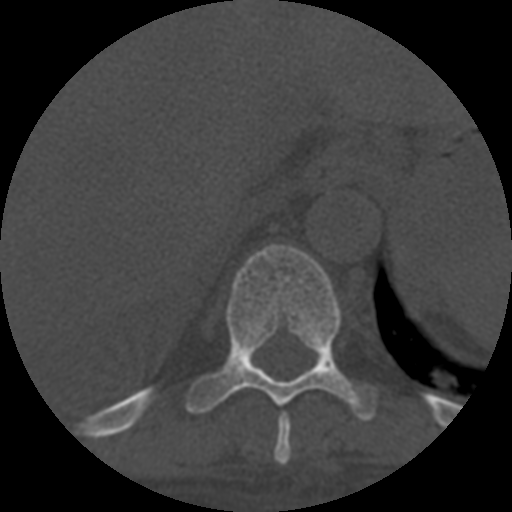
CT including the spine, one axial slice; slice 359 of 708 in the series (ordered by position); 120 kVp; one of 3 acquisitions stored at this slice position; bone window (W 1800 / L 400 HU); 512 × 512 image matrix. Patient age 55 years. From the clinical record (not read from this slice): primary cancer: colon; vertebrae with lytic lesions (as recorded): T12, L1, L5.
Structures marked on this image (semi-automatic segmentation, software-assisted and operator-edited):
- T10 vertebra: bounding box (x1, y1, x2, y2) in pixels: (186, 244, 379, 421)
- T9 vertebra: (274, 413, 291, 465)